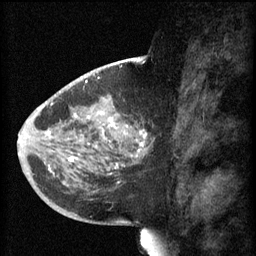
Breast MRI (dynamic contrast-enhanced), one sagittal slice; slice 28 of 60 in the series (ordered by position); 3 images stored at this slice position (order not interpretable as contrast timing); 1.5 T; TE 4.2 ms, TR 8.1 ms; 2 mm slice thickness; 256 × 256 image matrix, field of view 200 × 200 mm. Female patient, age 44 years.
Outlined on this slice (semi-automatic segmentation, software-assisted and operator-edited):
- analysis volume of interest (the breast-tissue region the enhancement analysis was run in; not a lesion): bounding box <59,110,151,169> (left, top, right, bottom; pixels)
- tumour enhancement mask (voxels above the 70 % enhancement threshold inside the analysis volume of interest): <69,114,147,169>